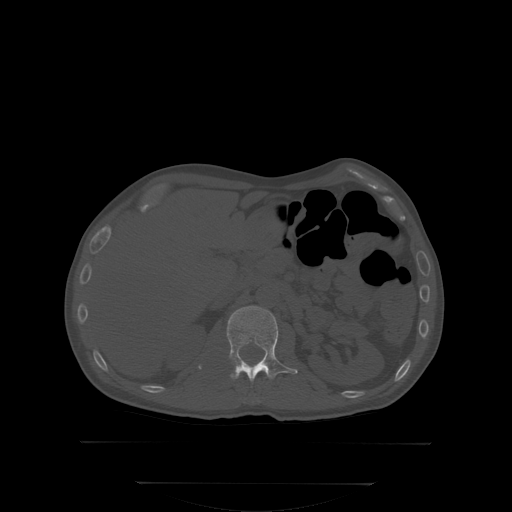
CT including the spine, one axial slice; slice 155 of 350 in the series (ordered by position); bone window (W 1800 / L 400 HU); 2.5 mm slice thickness; 512 × 512 image matrix. Male patient, age 58 years. From the clinical record (not read from this slice): primary cancer: prostate.
Annotated regions visible in this slice (semi-automatically segmented with operator editing):
- L1 vertebra: bounding box [x1, y1, x2, y2] px = [226, 305, 295, 381]
- T12 vertebra: [252, 401, 254, 403]